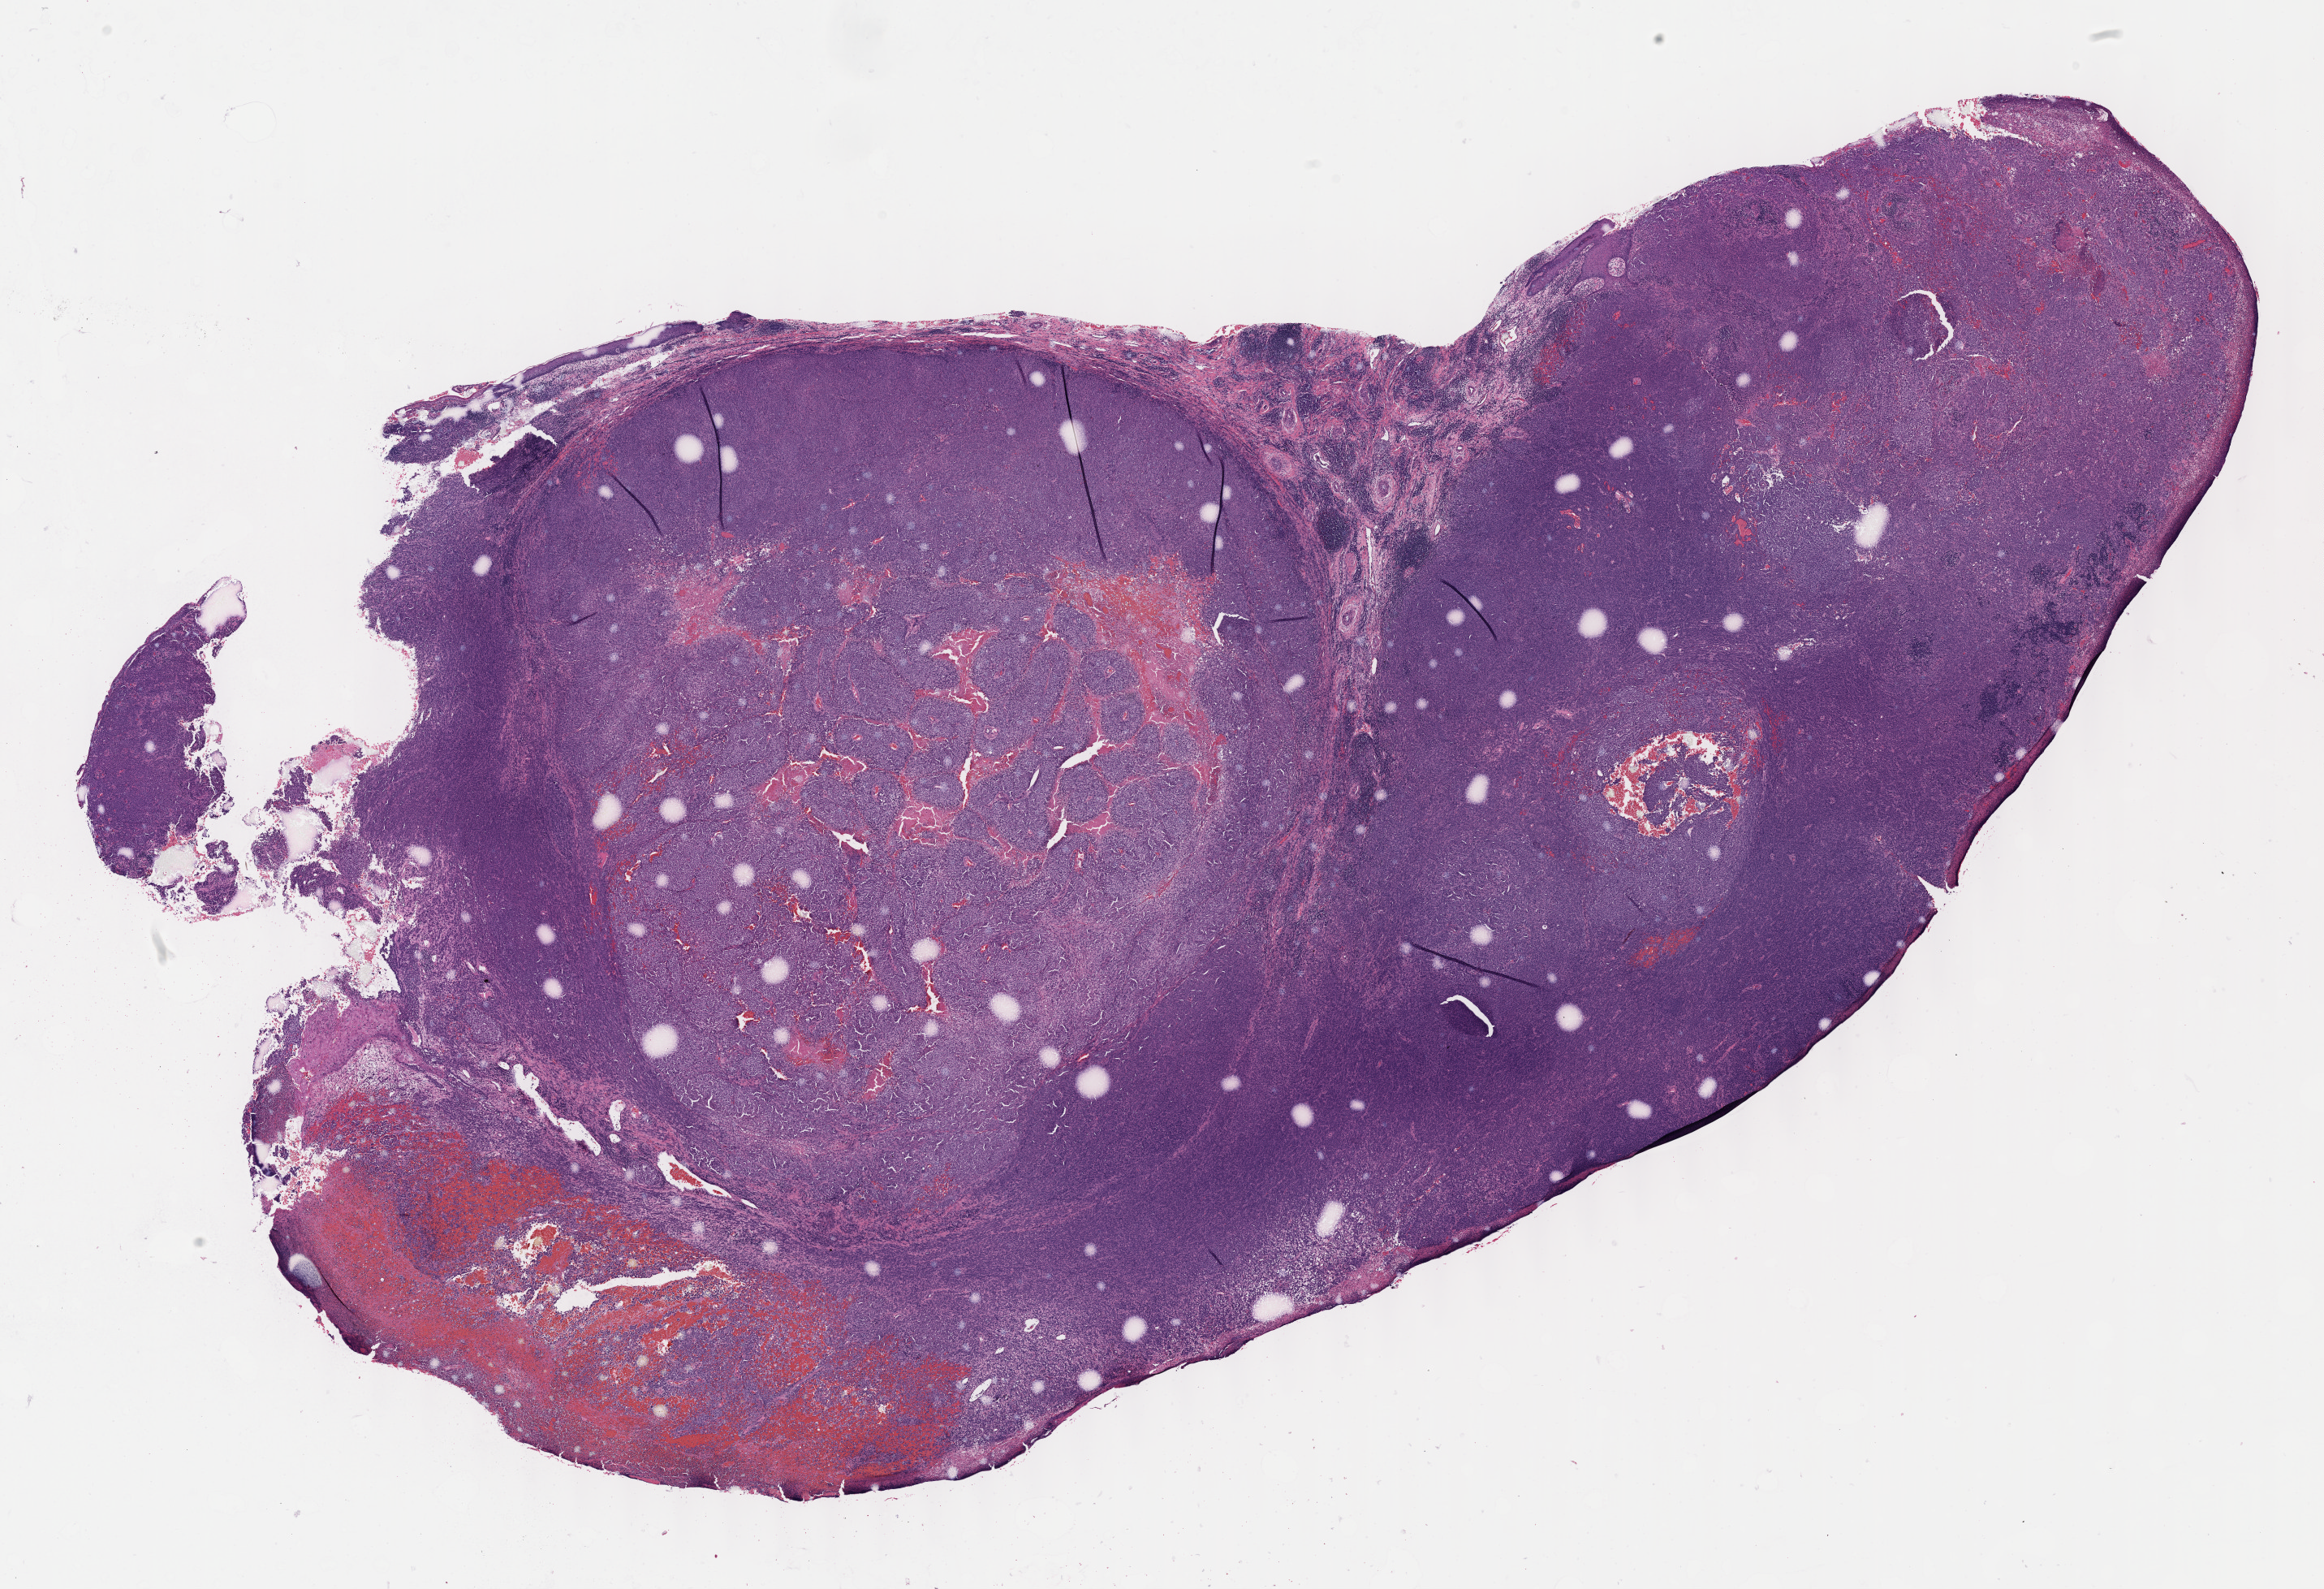
H&E-stained whole-slide image, a low-resolution overview of the entire scanned area, about 23.1 x 15.8 mm (acquisition: 40x scan). Formalin-fixed paraffin-embedded (FFPE) diagnostic section. Skin, primary tumour sample. Female, age 73 years at initial diagnosis.
- AJCC pathologic stage: IIC (7th edition)
- pathologic diagnosis: Amelanotic melanoma